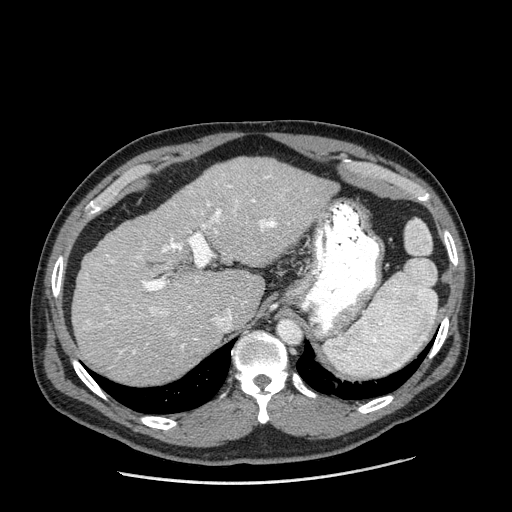
Contrast-enhanced abdominal CT (liver protocol), one axial slice. Position 133 of 198 along the scan axis. Reconstruction kernel STANDARD. One of 2 acquisitions stored at this slice position. Soft-tissue window (W 400 / L 40 HU). 2.5 mm slice thickness. 512 × 512 image matrix, field of view 400 × 400 mm. Case-level facts recorded for this patient, not image findings: diagnosis: hepatocellular carcinoma (patient treated with transarterial chemoembolisation; whether this scan precedes or follows treatment is not stated here); TNM stage (as recorded): Stage-II; Child-Pugh class: A; tumour differentiation: moderately differentiated; tumour size: 2.6 cm.
Structures marked on this image (semi-automatic segmentation, software-assisted and operator-edited):
- liver parenchyma outside the tumour (the mass and vessels are separate outlines, so this box may not span the whole liver): box from (x=72, y=156) to (x=336, y=384) px
- liver vessels: (x=86, y=175)–(x=277, y=354)